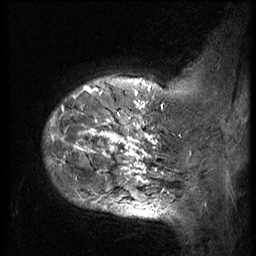
Breast MRI (dynamic contrast-enhanced), one sagittal slice. 3 images stored at this slice position (order not interpretable as contrast timing). 1.5 T. TE 4.2 ms, TR 9 ms. 2.5 mm slice thickness. 256 × 256 image matrix, field of view 180 × 180 mm. Female patient, age 49 years. Case-level facts recorded for this patient, not image findings: setting: breast cancer imaged before/during neoadjuvant chemotherapy; receptor status: HER2-positive.
Annotated regions visible in this slice (semi-automatically segmented with operator editing):
- analysis volume of interest (the breast-tissue region the enhancement analysis was run in; not a lesion): box from (x=42, y=85) to (x=168, y=207) px
- tumour enhancement mask (voxels above the 140 % enhancement threshold inside the analysis volume of interest): (x=47, y=86)–(x=164, y=204)